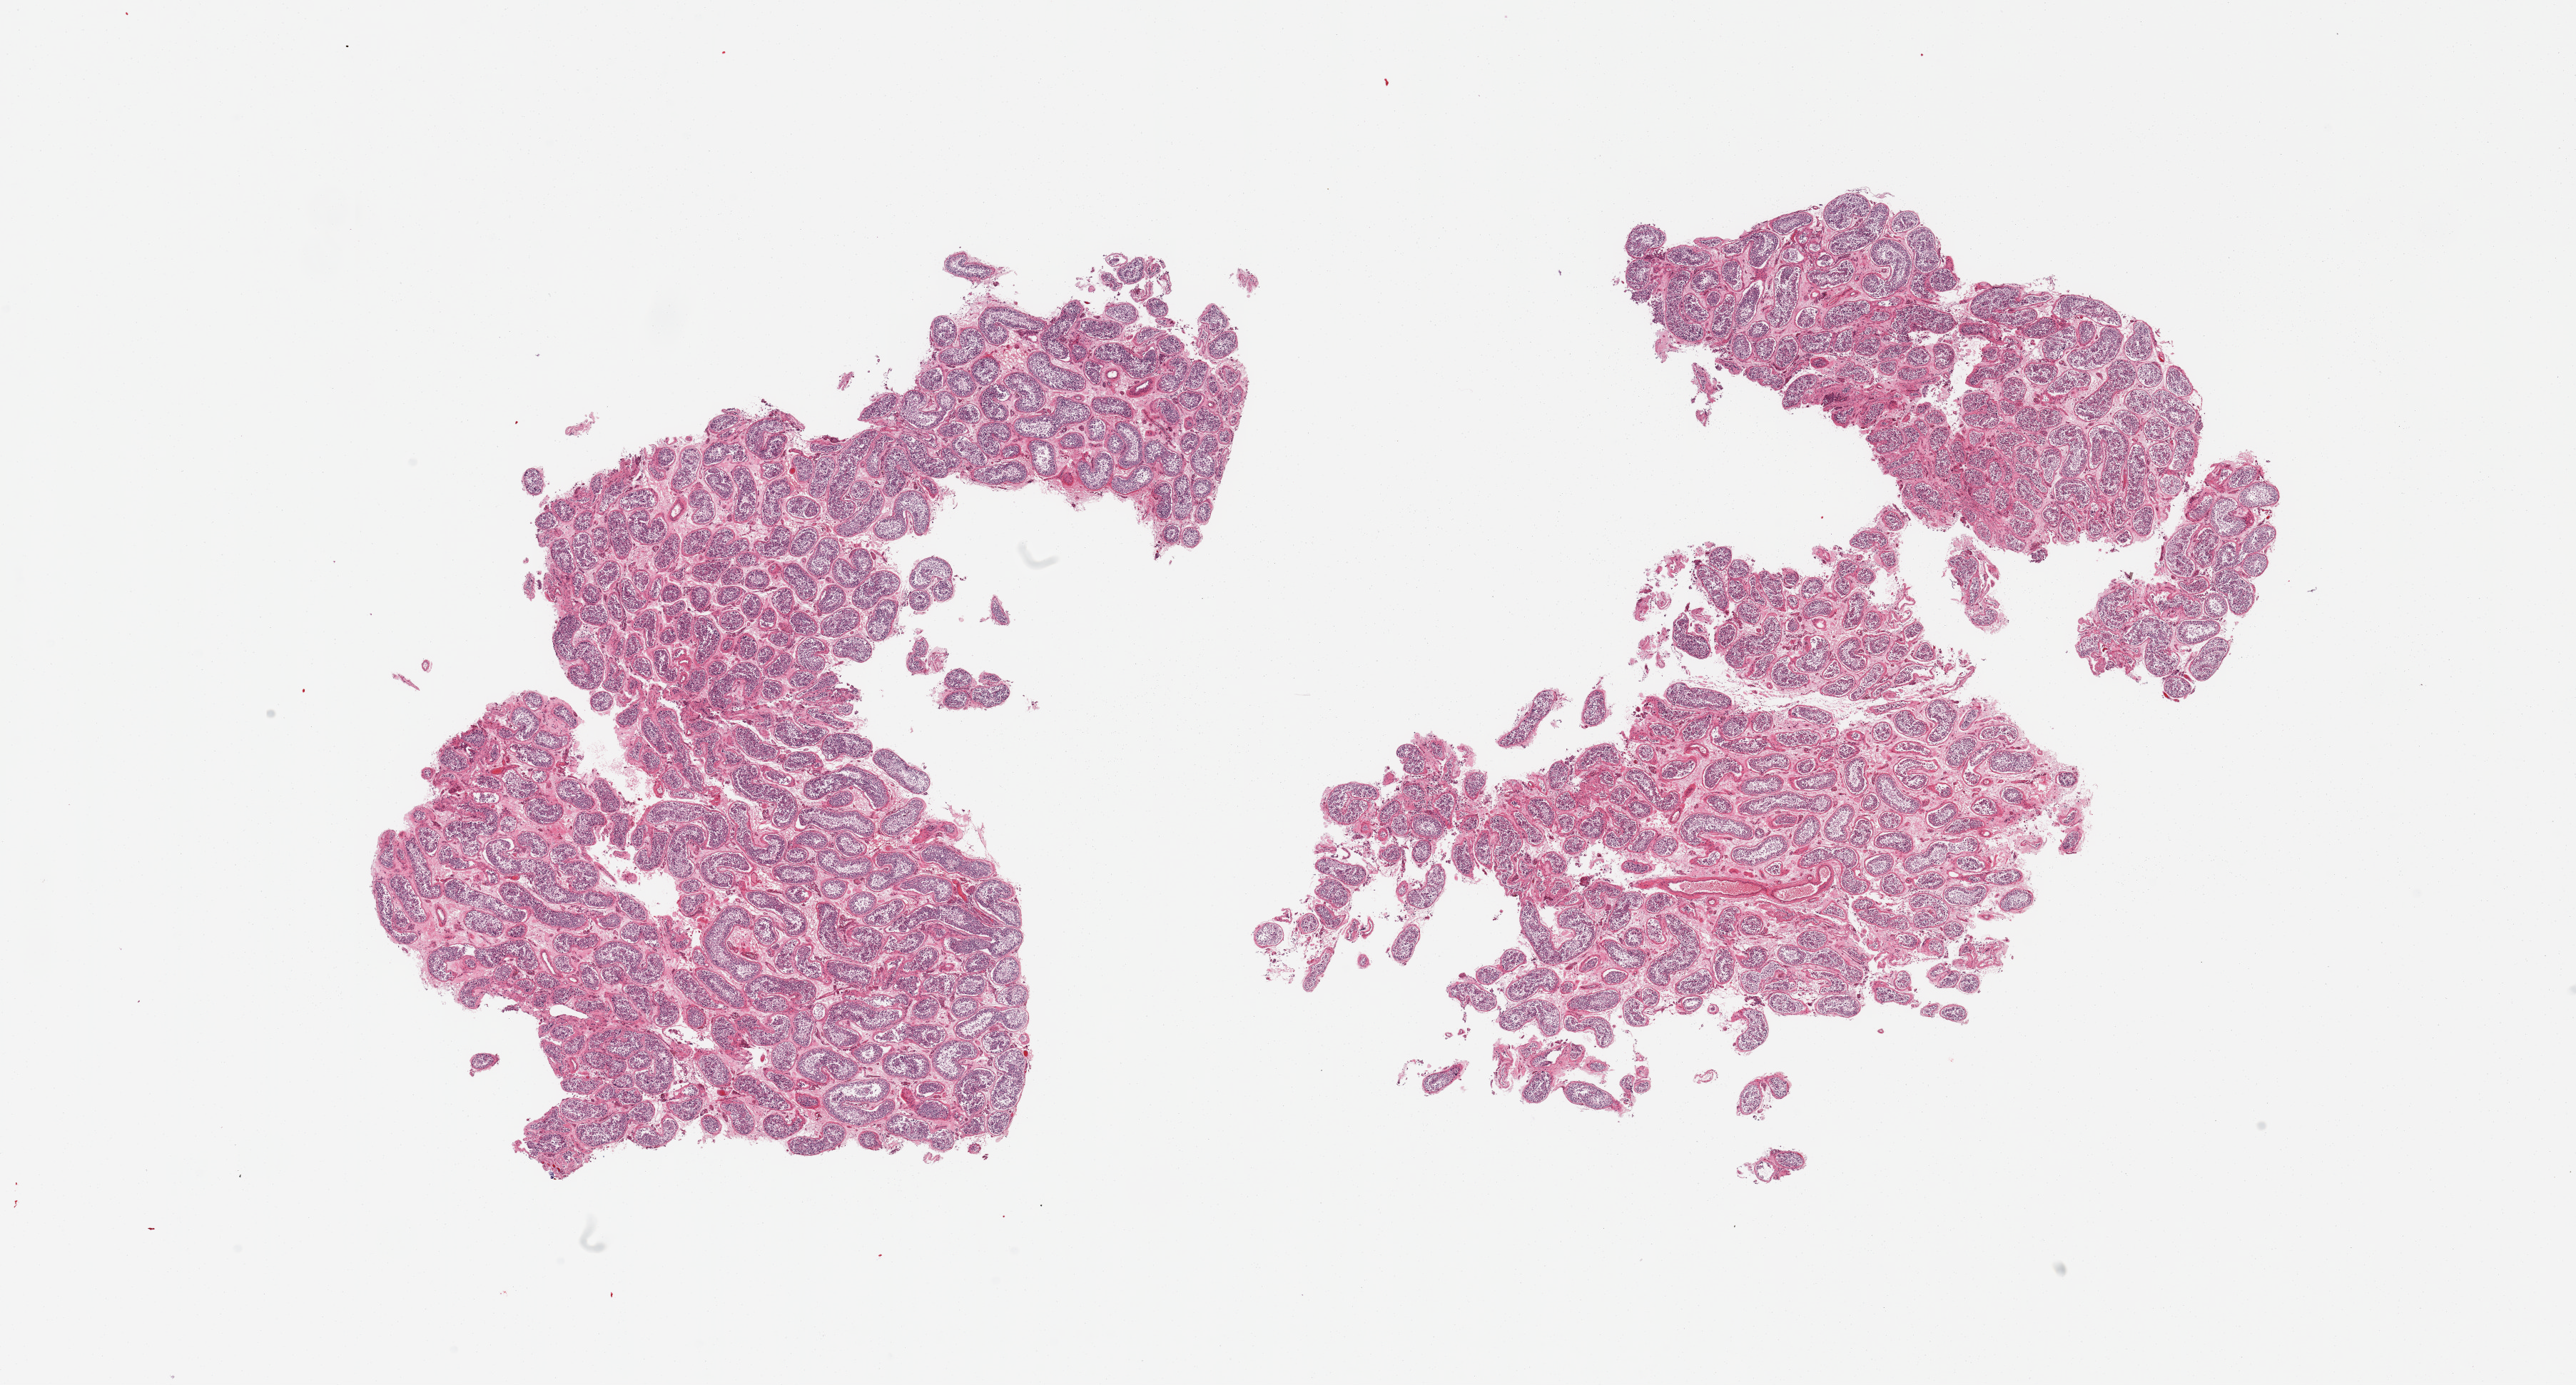
Whole-slide image, hematoxylin and eosin (H&E) stain, brightfield, shown as a low-resolution overview of the whole scanned area (about 28.5 x 15.3 mm), PAXgene-fixed paraffin-embedded (PFPE) section, sampled site (target tissue): testis, tissue donor sample. Male donor.
* pathologist's review note for this sample: 2 pieces, spermatogenesis present